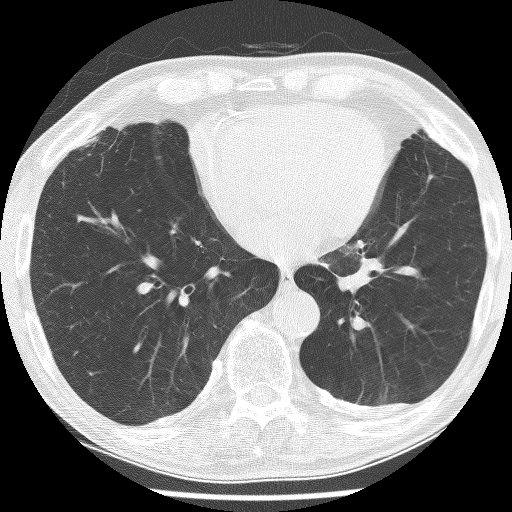
Low-dose screening chest CT, axial slice; baseline annual screen; lung window (W 1500 / L -600 HU); 2.5 mm slice thickness; 120 kVp; slice 162 of 226 in the series; 512 × 512 image matrix, field of view 320 × 320 mm. Male, age 74 years at enrolment.
- Lesion marked by an expert reader, bounding box (x1, y1, x2, y2) in pixels: (319, 234, 431, 329).
- Screening reader's record for this exam (one nodule recorded; not confirmed to be the boxed lesion): non-calcified nodule or mass ≥4 mm, left lower lobe, 30 × 27 mm, spiculated (stellate) margins, soft tissue attenuation.
- Official screen result: positive, change unspecified: nodule(s) >= 4 mm or enlarging nodule(s), mass(es), or other non-specific abnormalities suspicious for lung cancer.
- Later outcome: lung cancer diagnosed 151 days after this screen — adenocarcinoma, NOS, left lower lobe, stage IIIA (AJCC 6th edition), 49 mm at pathology.